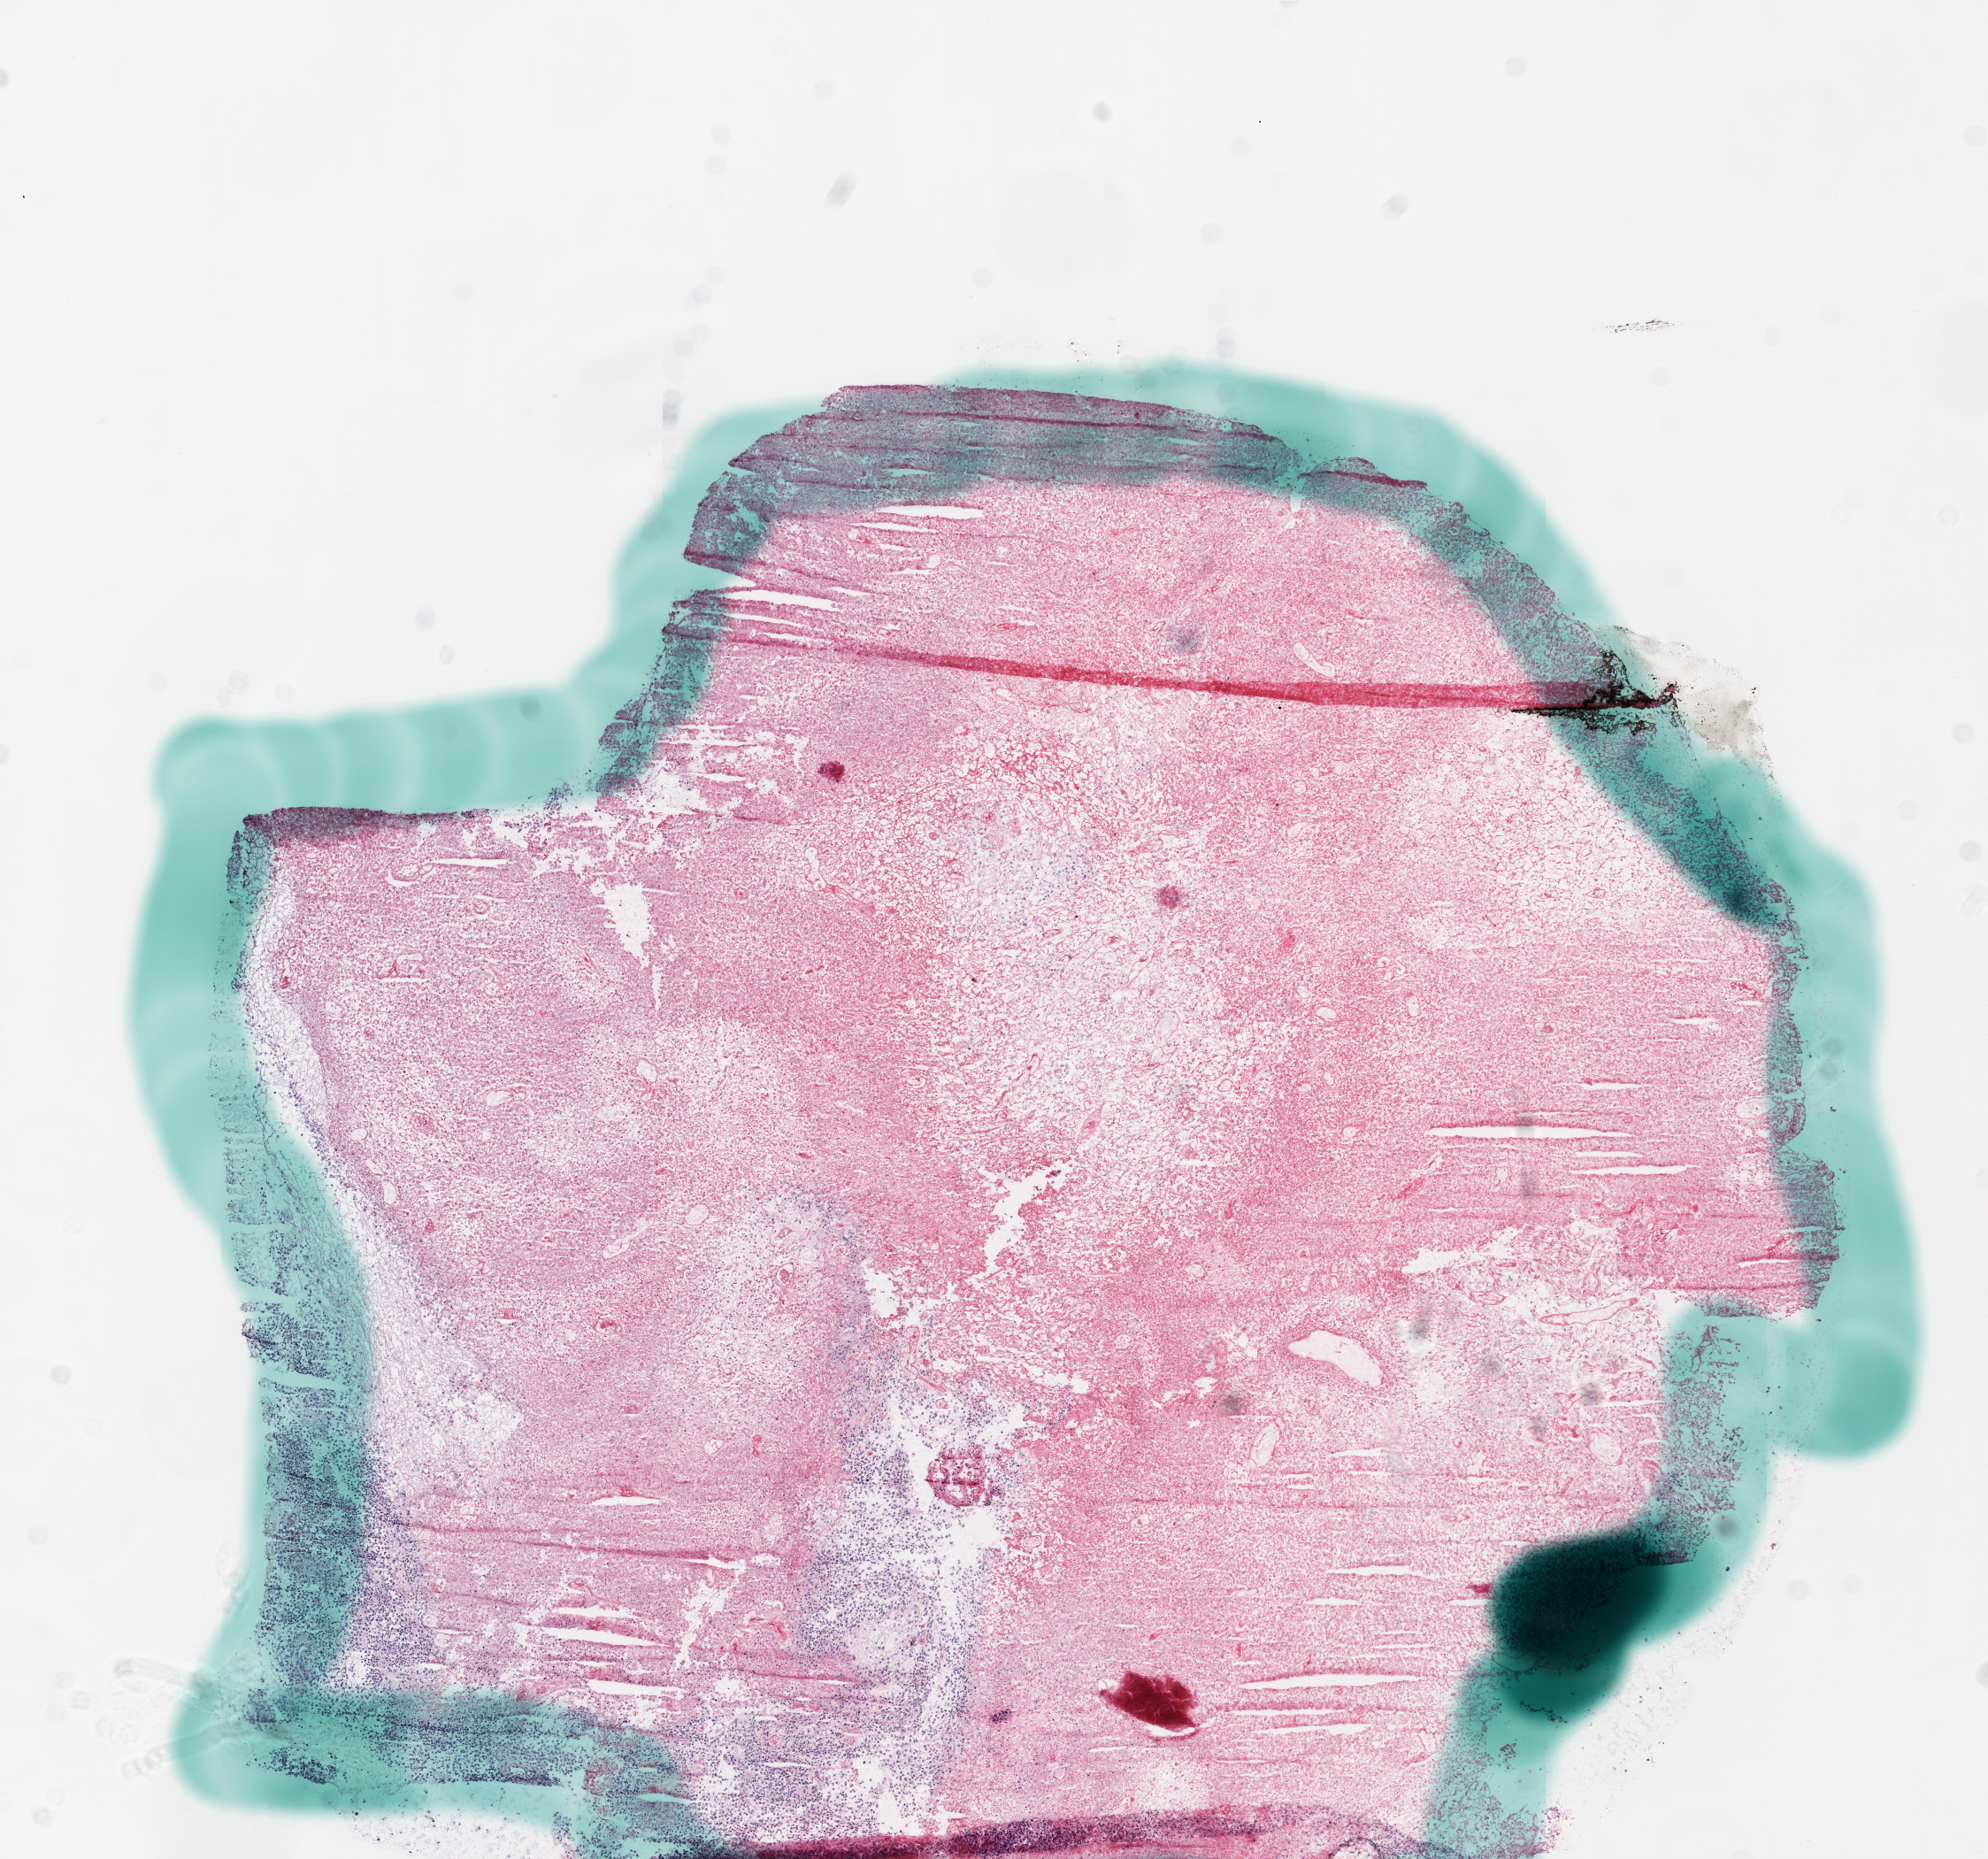
Whole-slide histology image, Hematoxylin and eosin (H&E) stained — shown as a low-resolution overview of the whole scanned area (about 9.0 x 8.4 mm). Frozen section from the bottom of the tissue portion. Primary tumour sample from the brain. Female, age 32 years at initial diagnosis. Pathologist review of this section (percent, as recorded): tumour cells 15%, tumour nuclei 100%, normal cells 0%, stromal cells 0%, necrosis 85%.
Histologic diagnosis: Glioblastoma.